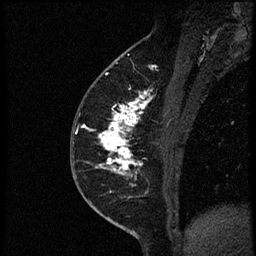
Breast MRI (dynamic contrast-enhanced), one sagittal slice; position 29 of 56 along the scan axis; dynamic contrast-enhanced study with each time point stored as its own series, time point 2 of 4 at this slice position (early post-contrast, ordered by acquisition time); 1.5 T; TE 4.2 ms, TR 18.9 ms; 2 mm slice thickness; 256 × 256 image matrix, field of view 200 × 200 mm. Female patient. Case-level facts recorded for this patient, not image findings: setting: breast cancer imaged before/during neoadjuvant chemotherapy; receptor status: HER2-positive.
Structures marked on this image (semi-automatic segmentation, software-assisted and operator-edited):
- analysis volume of interest (the breast-tissue region the enhancement analysis was run in; not a lesion): bounding box (x1, y1, x2, y2) in pixels: (78, 85, 174, 189)
- tumour enhancement mask (voxels above the 100 % enhancement threshold inside the analysis volume of interest): (83, 90, 153, 178)